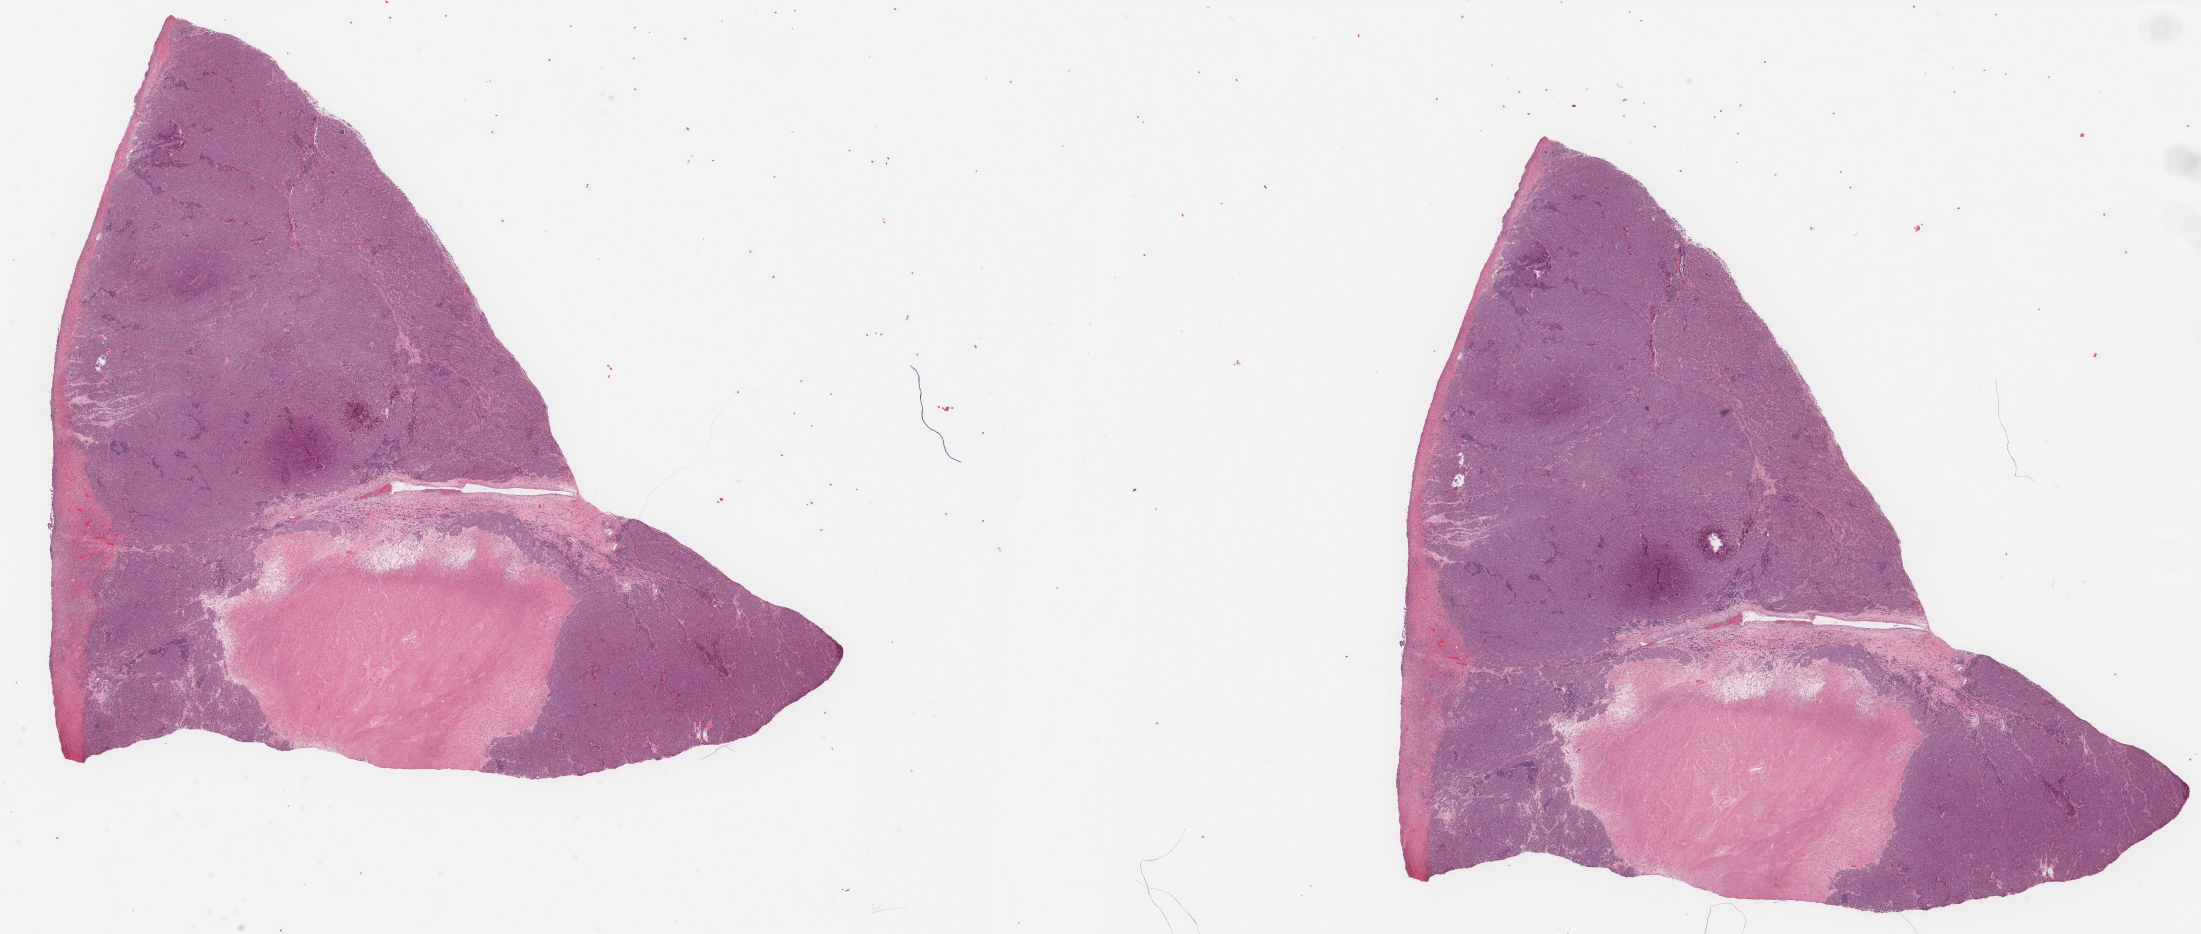
Whole-slide histology image, H&E-stained, a low-resolution overview of the entire scanned area, about 34.8 x 14.8 mm (acquisition: 40x scan). FFPE section. Sample: primary tumour, skin. Male, age 69 years at initial diagnosis.
• diagnosis: Nodular melanoma
• AJCC pathologic stage: IIC
• TNM: T4b N0 M0